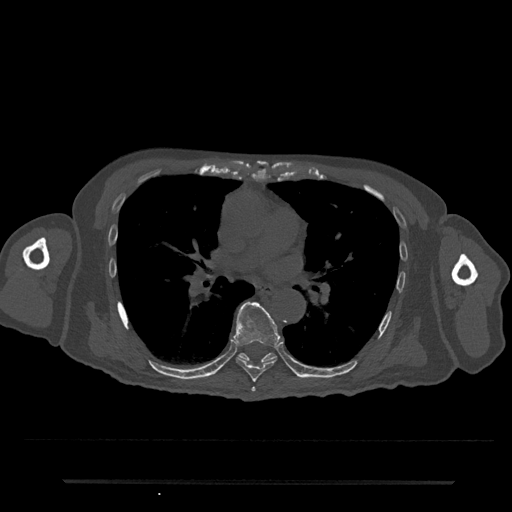
CT including the spine, one axial slice. Slice 462 of 797 in the series (ordered by position). Reconstruction kernel Br40s/3. 120 kVp. Bone window (W 1800 / L 400 HU). 512 × 512 image matrix, field of view 427 × 427 mm. Patient: male, 74 years. From the clinical record (not read from this slice): primary cancer: prostate.
Structures marked on this image (semi-automatically segmented with operator editing):
- T6 vertebra: bounding box (x1, y1, x2, y2) in pixels: (251, 387, 256, 392)
- T7 vertebra: (233, 301, 281, 382)
- T8 vertebra: (238, 353, 276, 363)